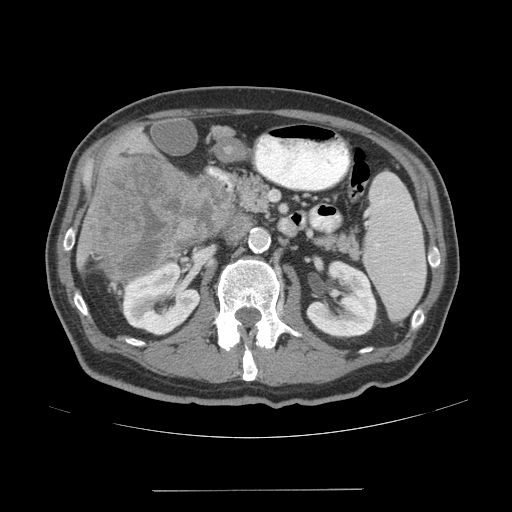
Contrast-enhanced abdominal CT (liver protocol), one axial slice. Position 15 of 77 along the scan axis. Reconstruction kernel STANDARD. 140 kVp. Soft-tissue window (W 400 / L 40 HU). 2.5 mm slice thickness. 512 × 512 image matrix. From the clinical record (not read from this slice): diagnosis: hepatocellular carcinoma (patient treated with transarterial chemoembolisation; whether this scan precedes or follows treatment is not stated here); TNM stage (as recorded): Stage-IVA; Child-Pugh class: A; tumour differentiation: well differentiated; tumour nodularity: uninodular.
Annotated regions visible in this slice (semi-automatically segmented with operator editing):
- liver parenchyma outside the tumour (the mass and vessels are separate outlines, so this box may not span the whole liver): bounding box [x1, y1, x2, y2] px = [76, 134, 171, 290]
- mass: [87, 151, 229, 279]